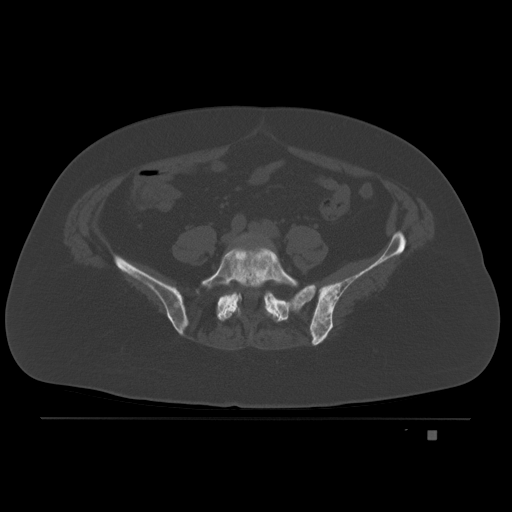
CT including the spine, one axial slice. Position 30 of 221 along the scan axis. Bone window (W 1800 / L 400 HU). 3 mm slice thickness. 512 × 512 image matrix, field of view 474 × 474 mm. Patient: female, 63 years. From the clinical record (not read from this slice): primary cancer: breast.
Outlined on this slice (semi-automatic segmentation, software-assisted and operator-edited):
- L4 vertebra: bounding box [x1, y1, x2, y2] px = [234, 233, 267, 243]
- L5 vertebra: [201, 247, 299, 322]